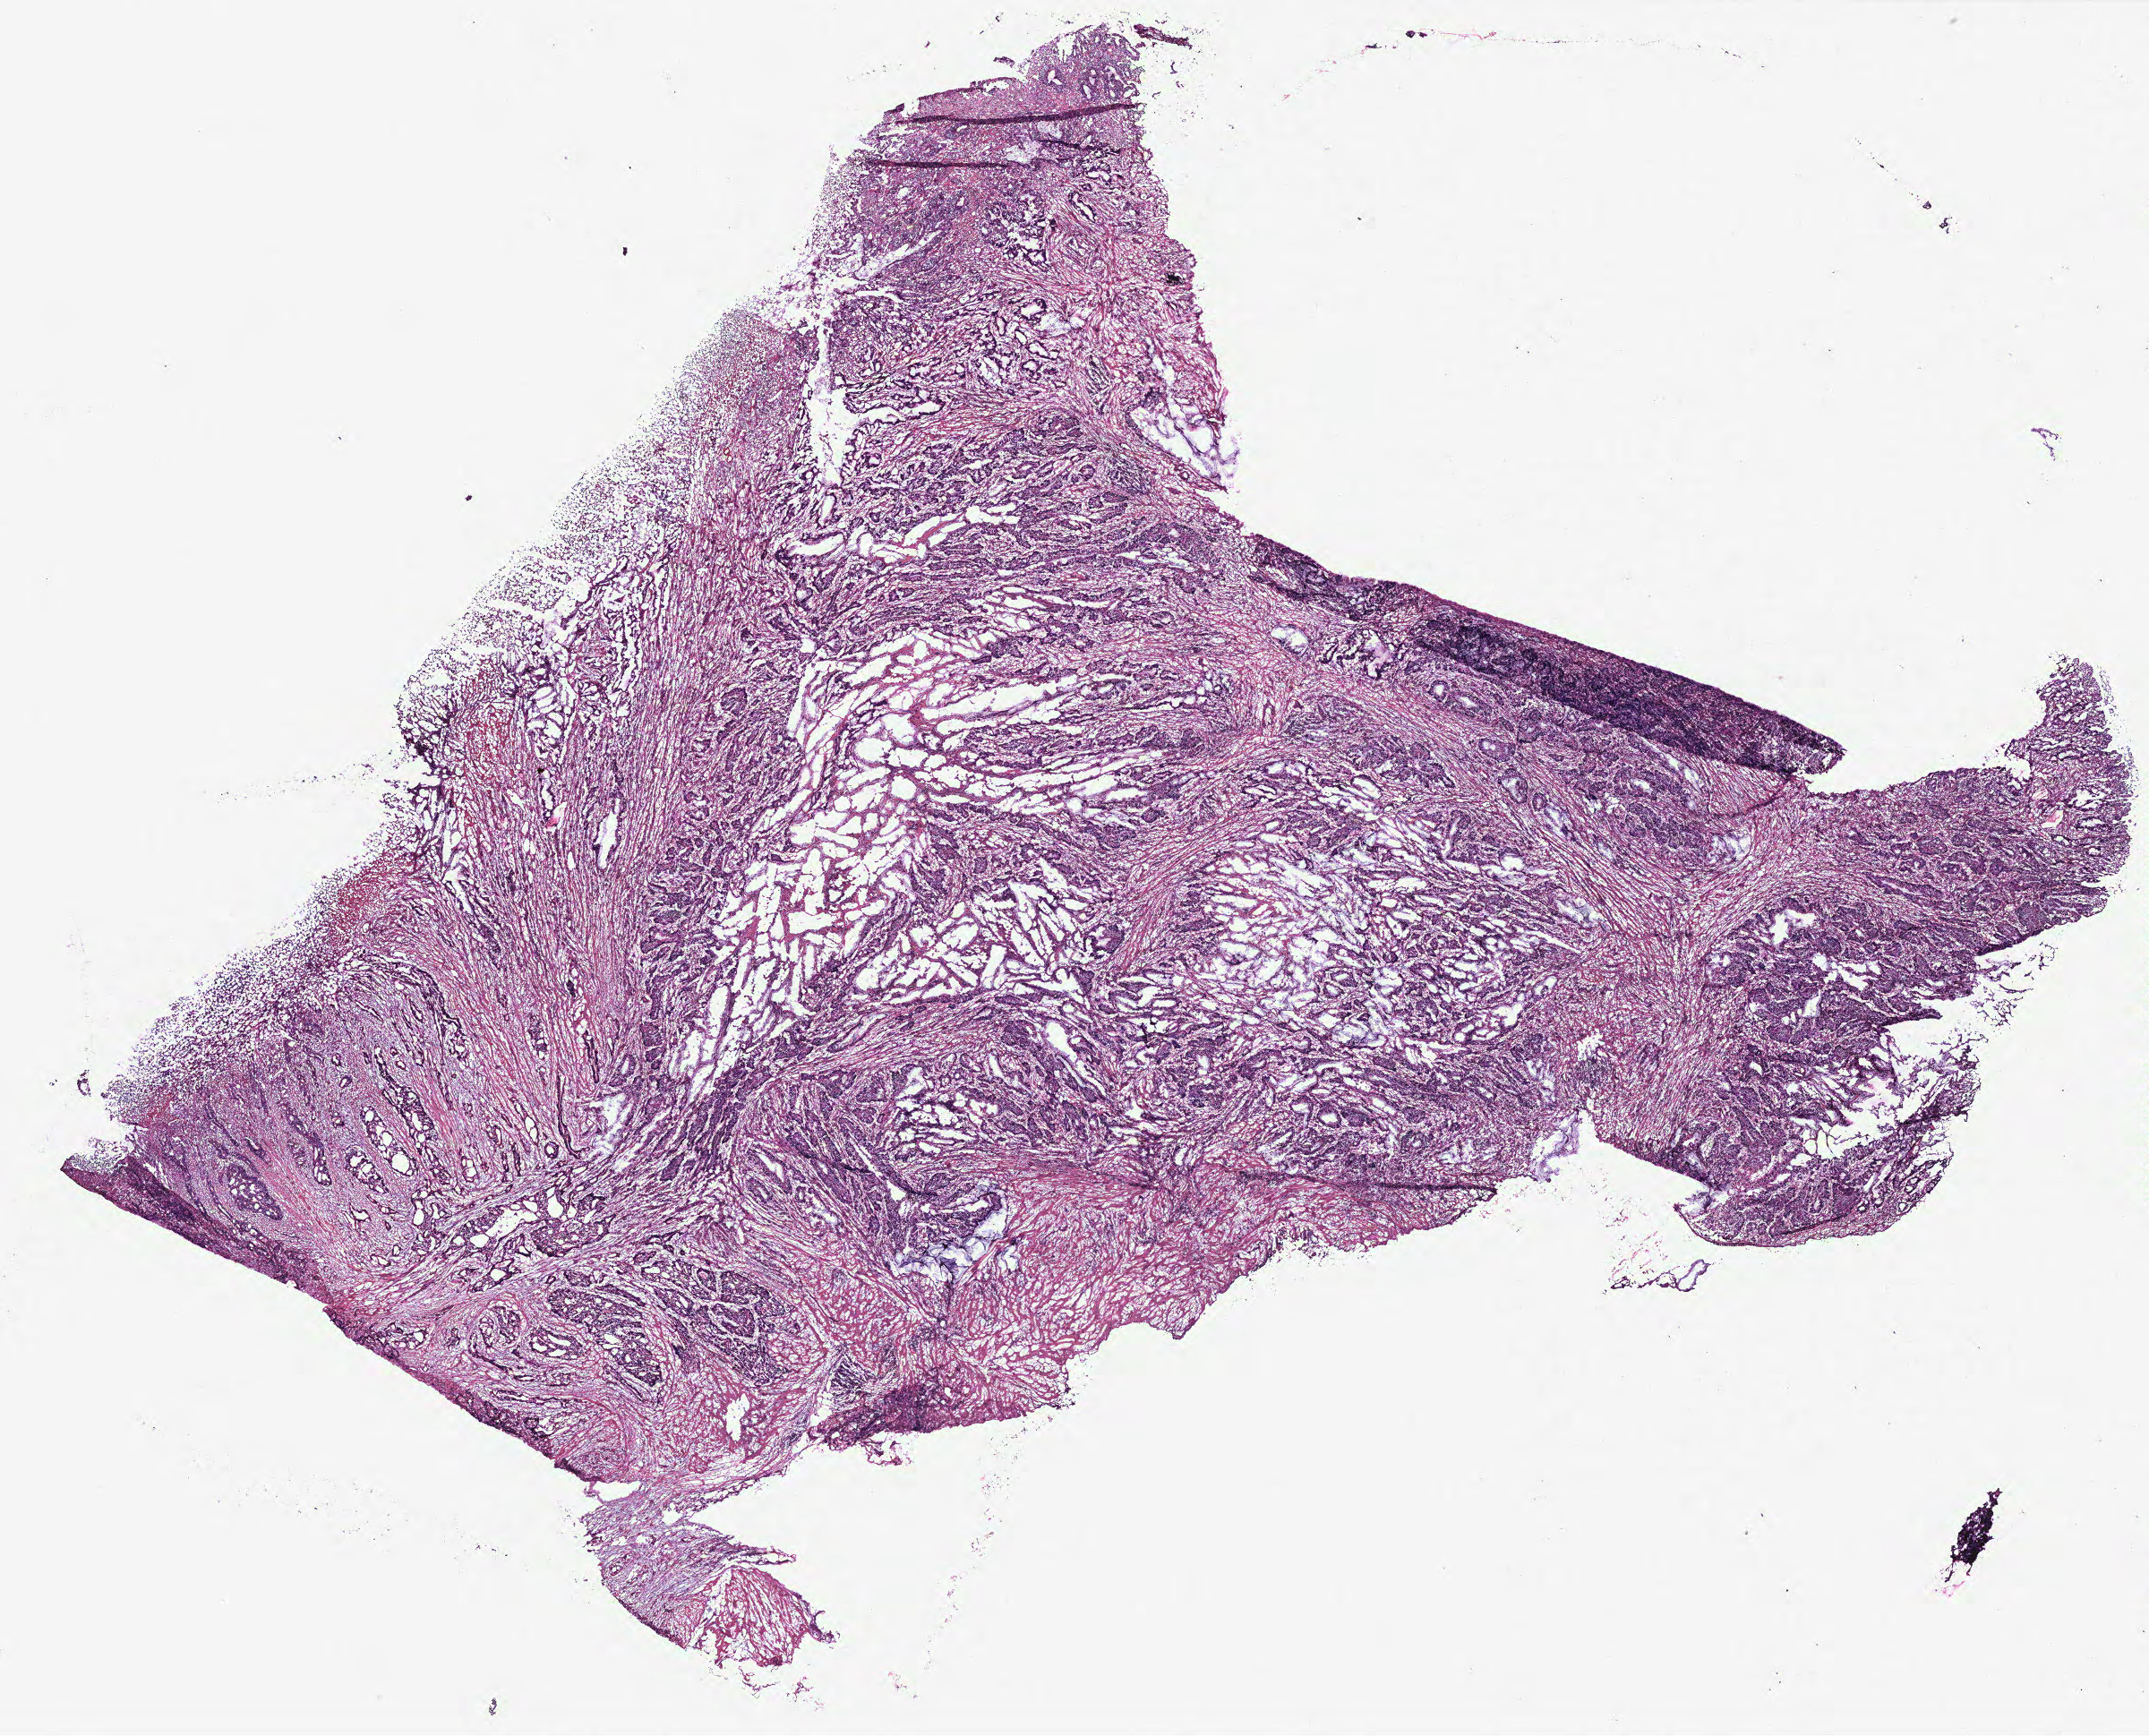
Whole-slide histology image, H&E-stained — low-resolution overview of the scanned area, about 19.2 x 15.5 mm; normal (non-tumour) tissue sample, colon. Female, 66 y/o.
• this section: normal (non-tumour) tissue from the same patient
• patient diagnosis: Adenocarcinoma, NOS